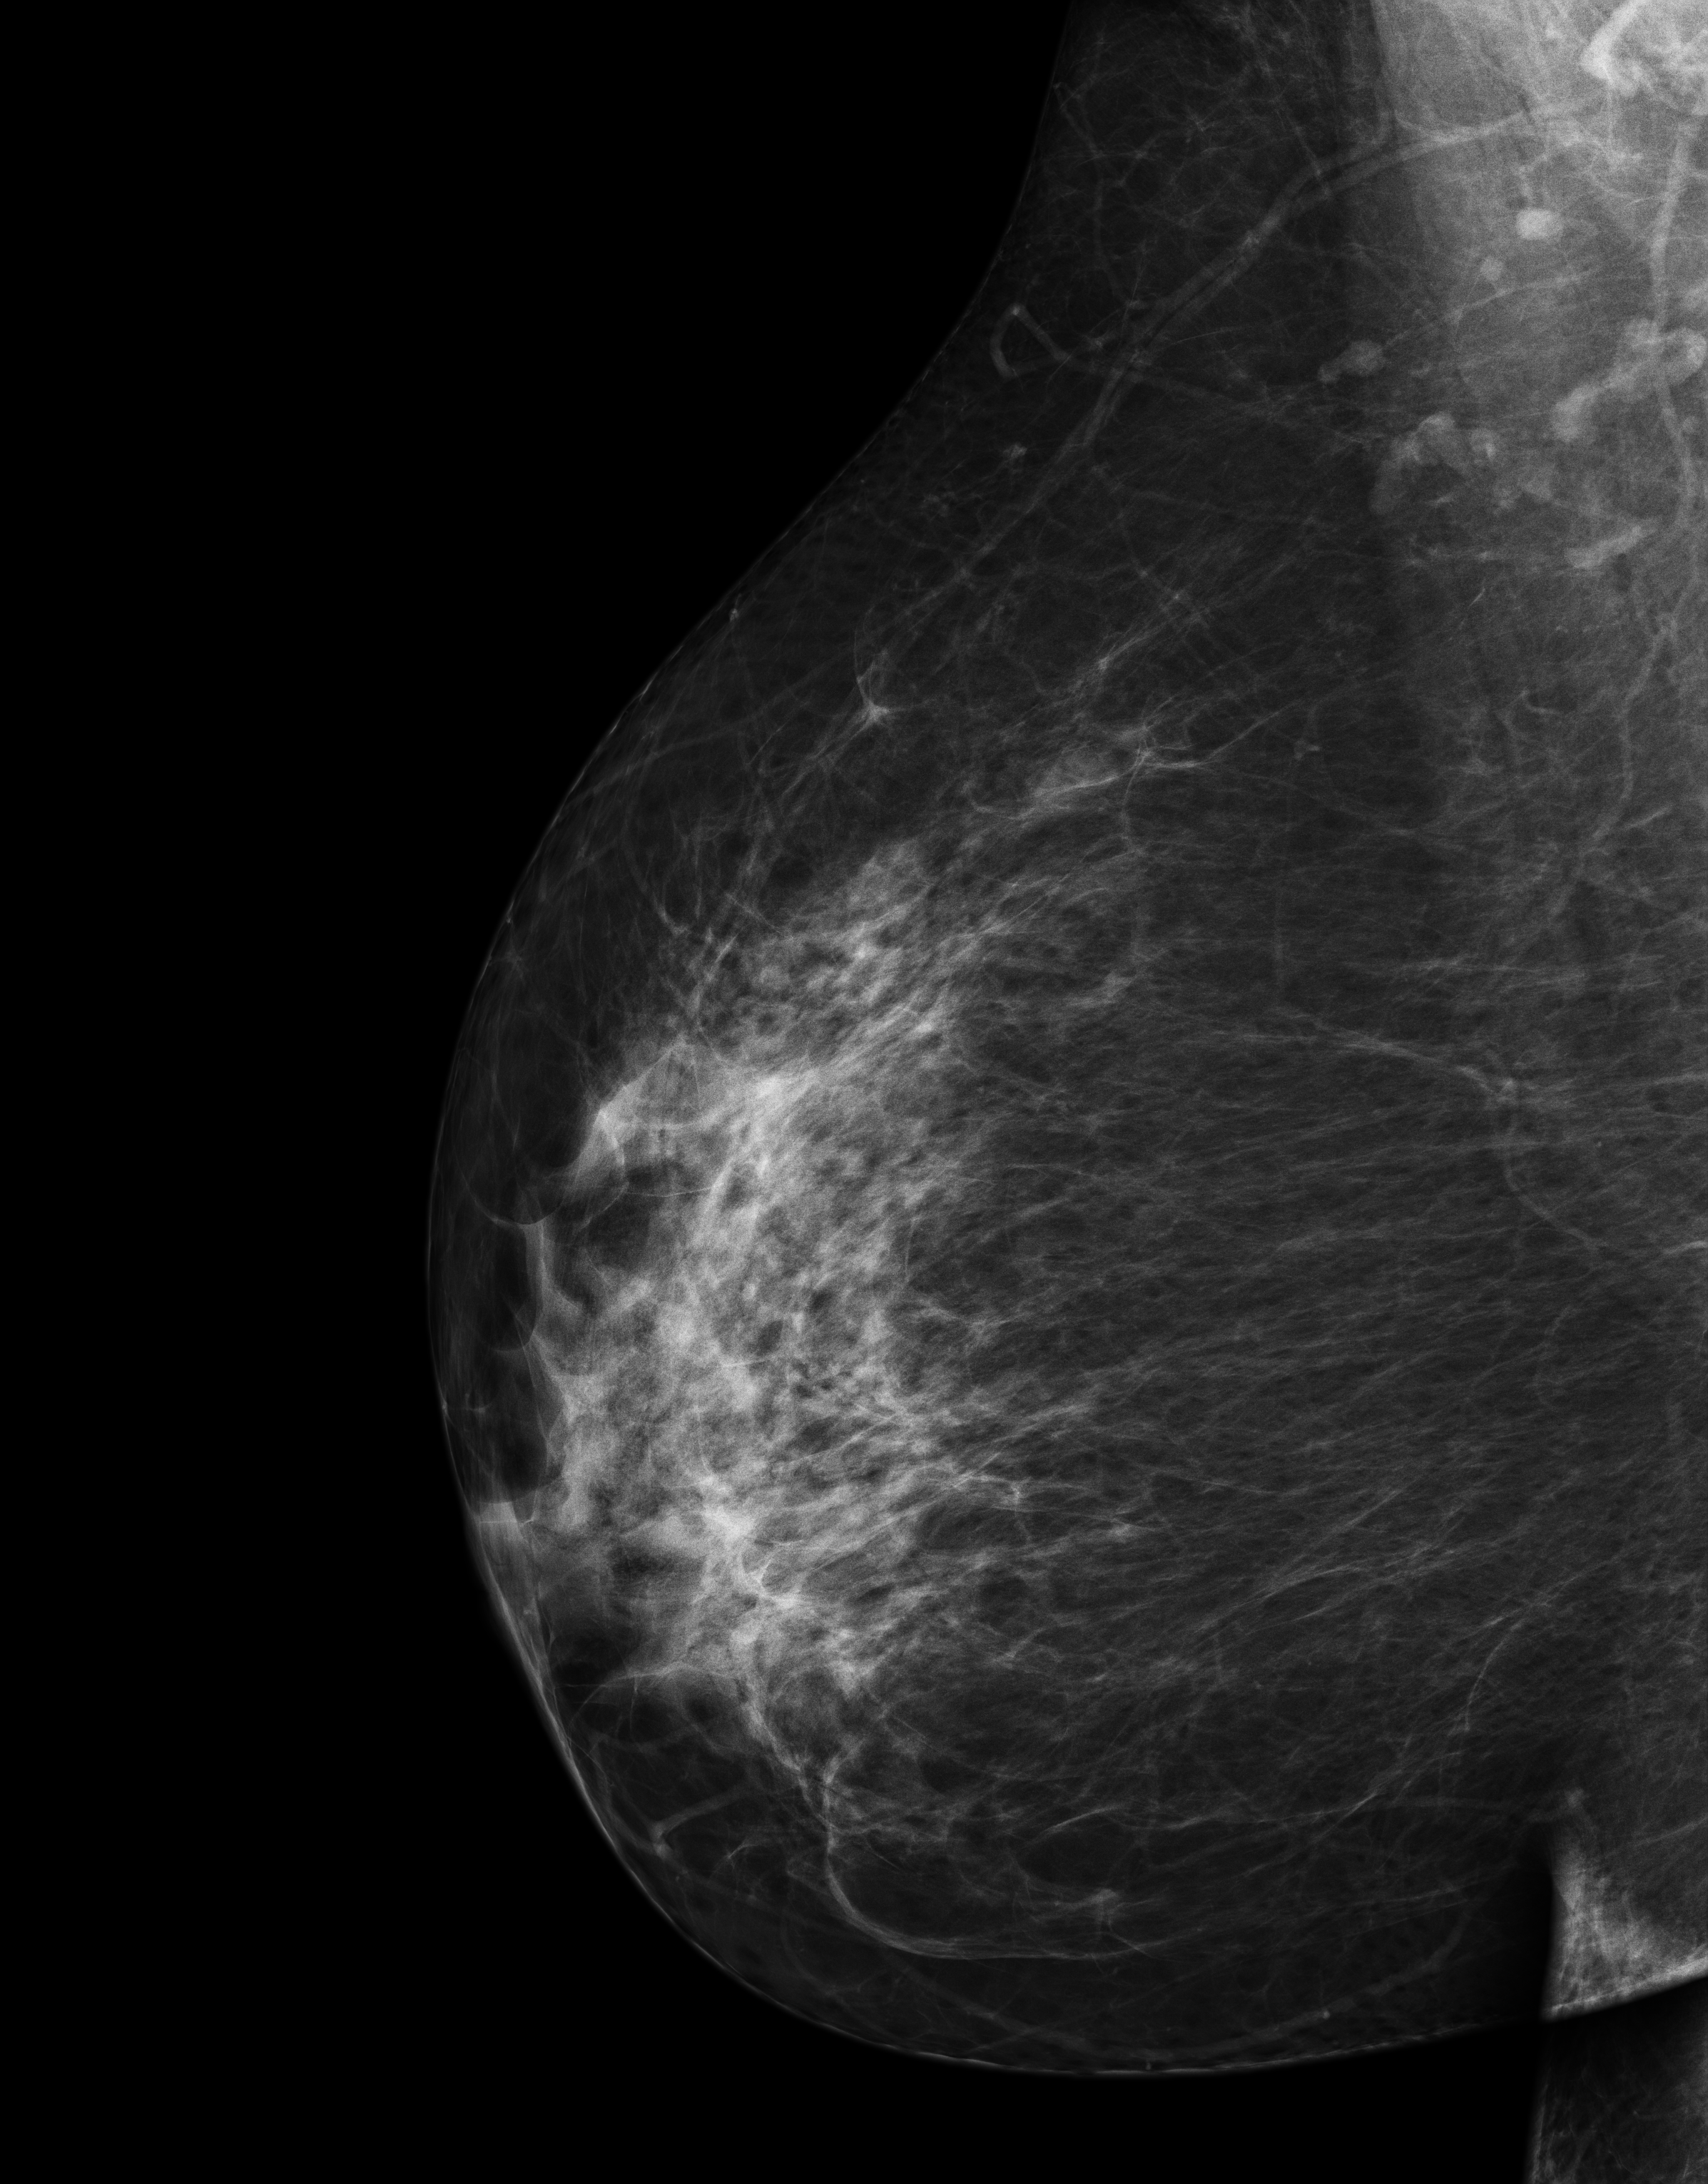
Digital mammogram (FFDM); right breast; medio-lateral oblique projection; annual screening mammography examination; compressed breast thickness 77 mm. Patient aged 56 years (female).
BI-RADS breast density category at the screening exam (both breasts, scale 1–4): 3. Final BI-RADS category for the screening round (tomosynthesis exam, both breasts): category 1. Recall: no recall after this screen.